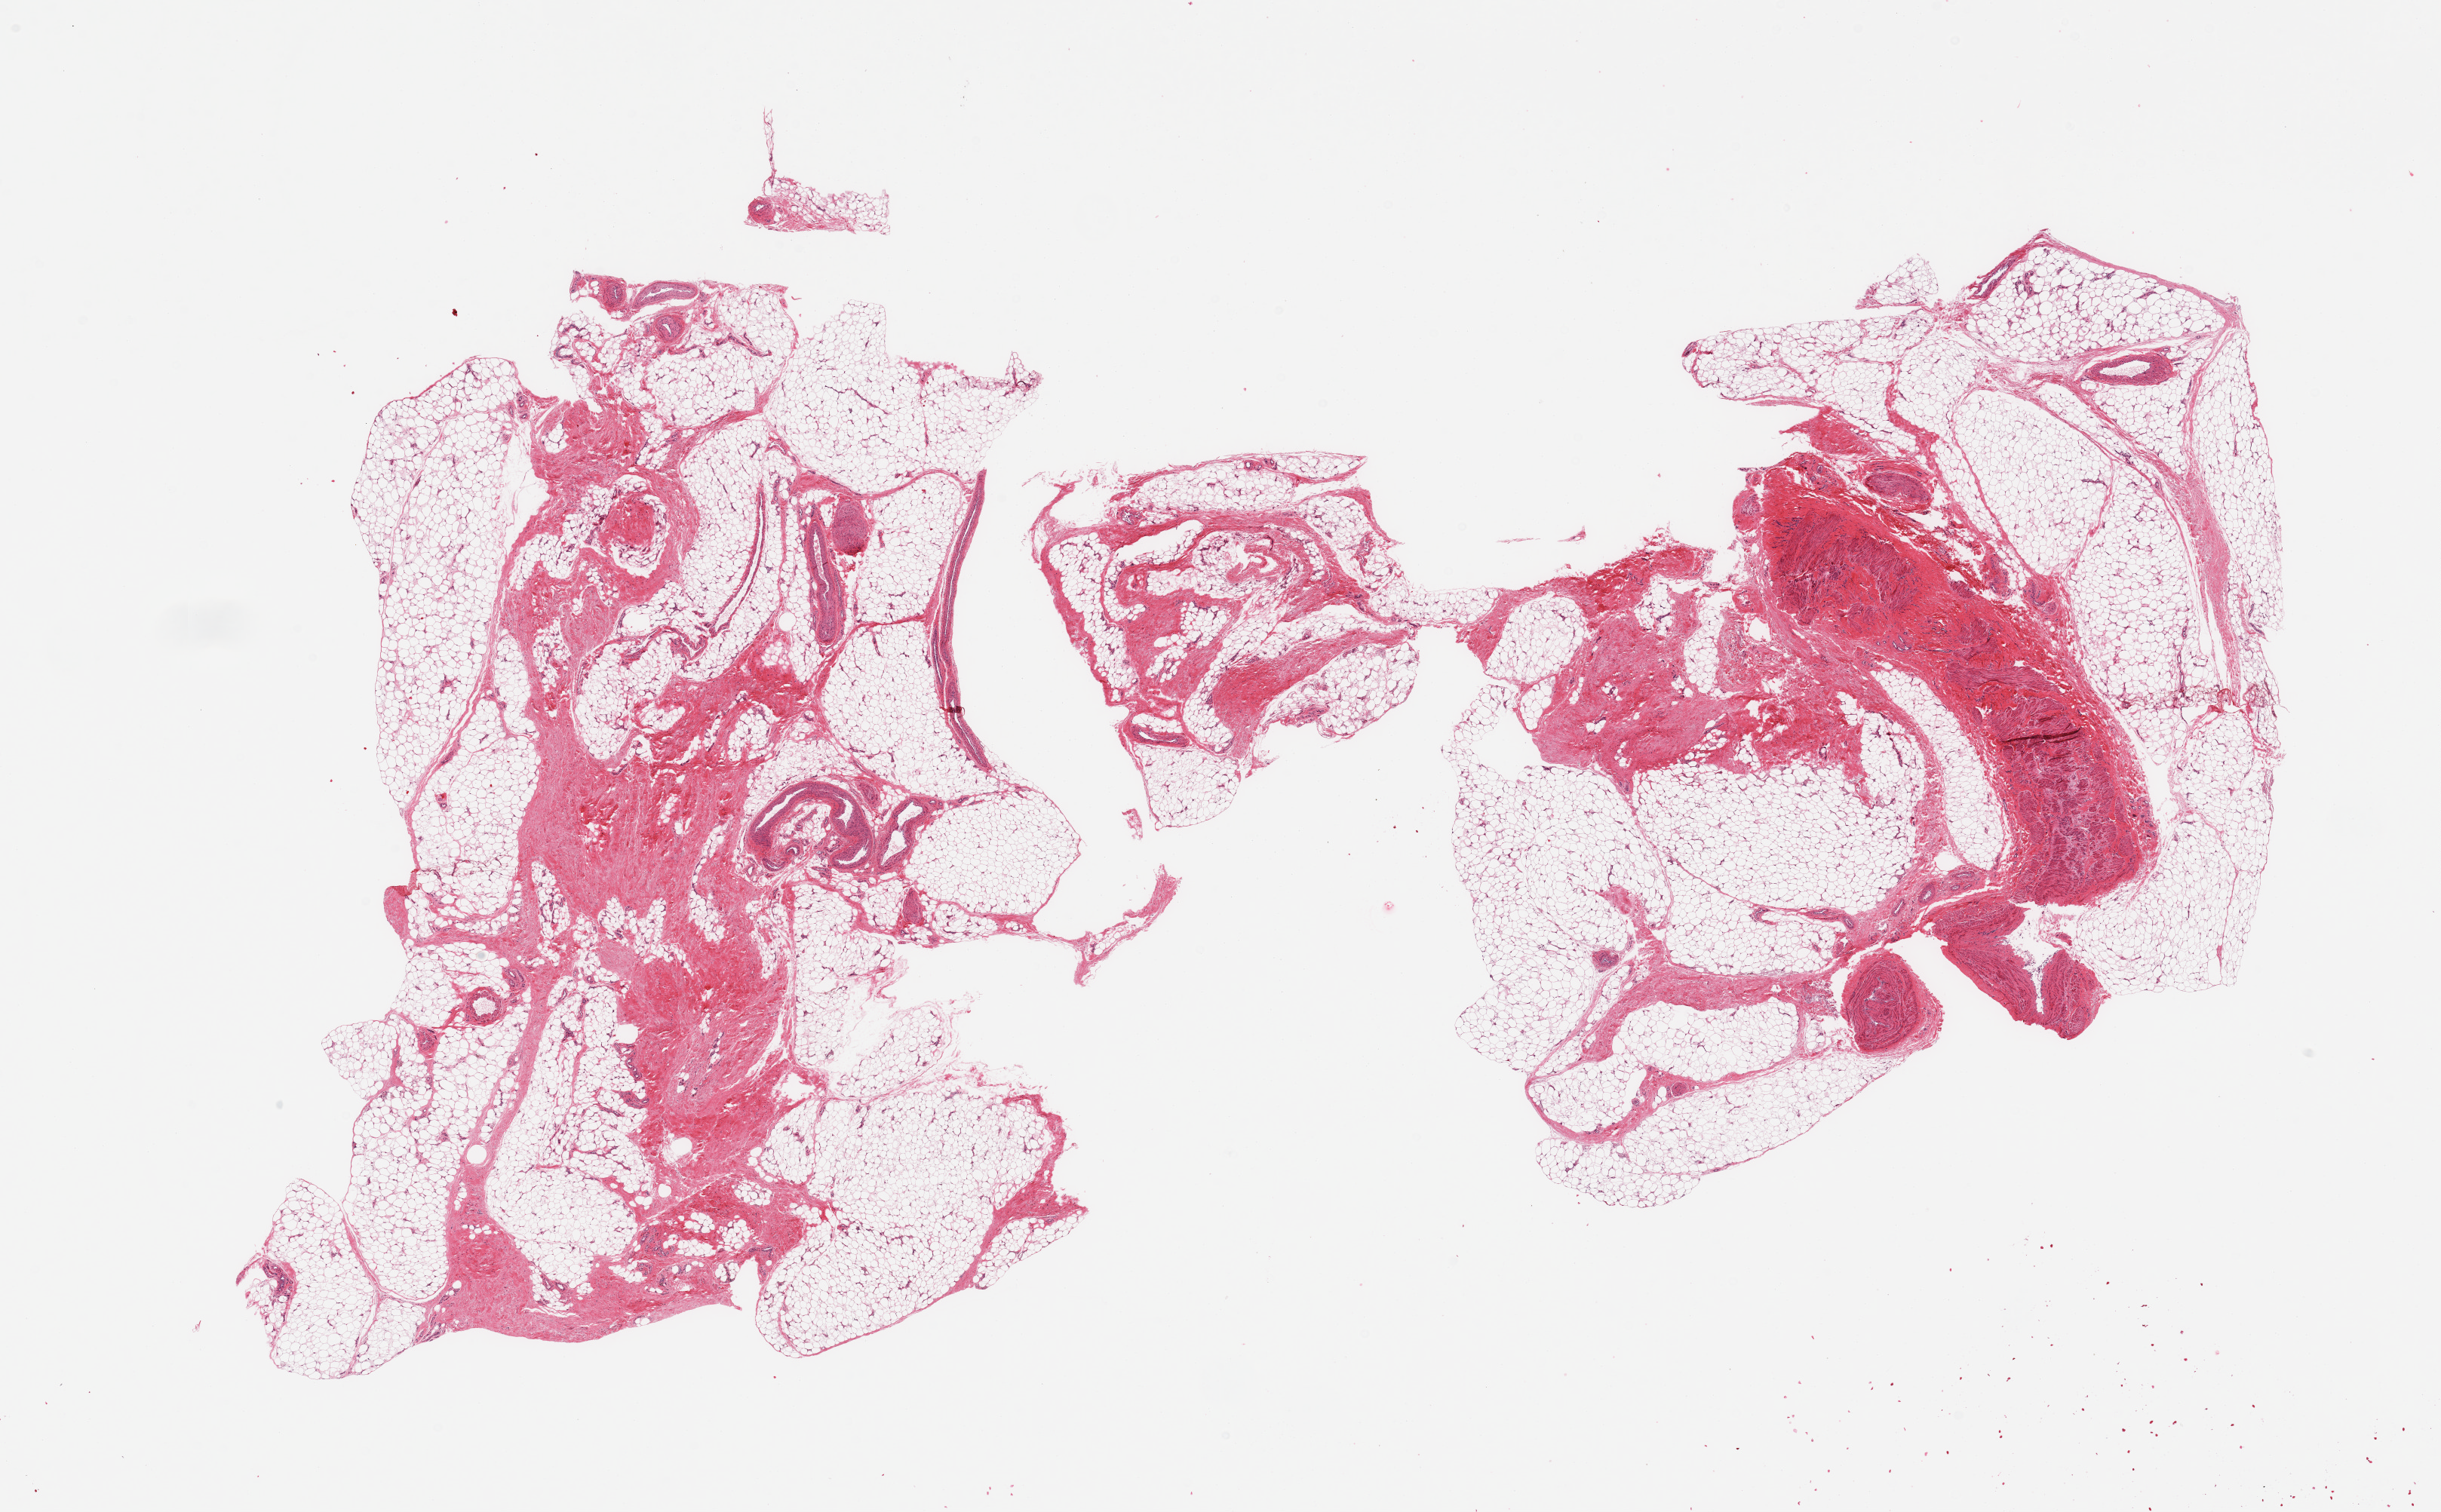
Digitized H&E-stained section, brightfield, low-resolution overview of the scanned area, about 25.6 x 15.9 mm (from a 20x scan). PAXgene-fixed paraffin-embedded (PFPE) section. Target tissue: adipose tissue. Donor tissue sample. Donor sex: female.
Review note (as recorded): 2 pieces, ~40% fascia/vacular elements.